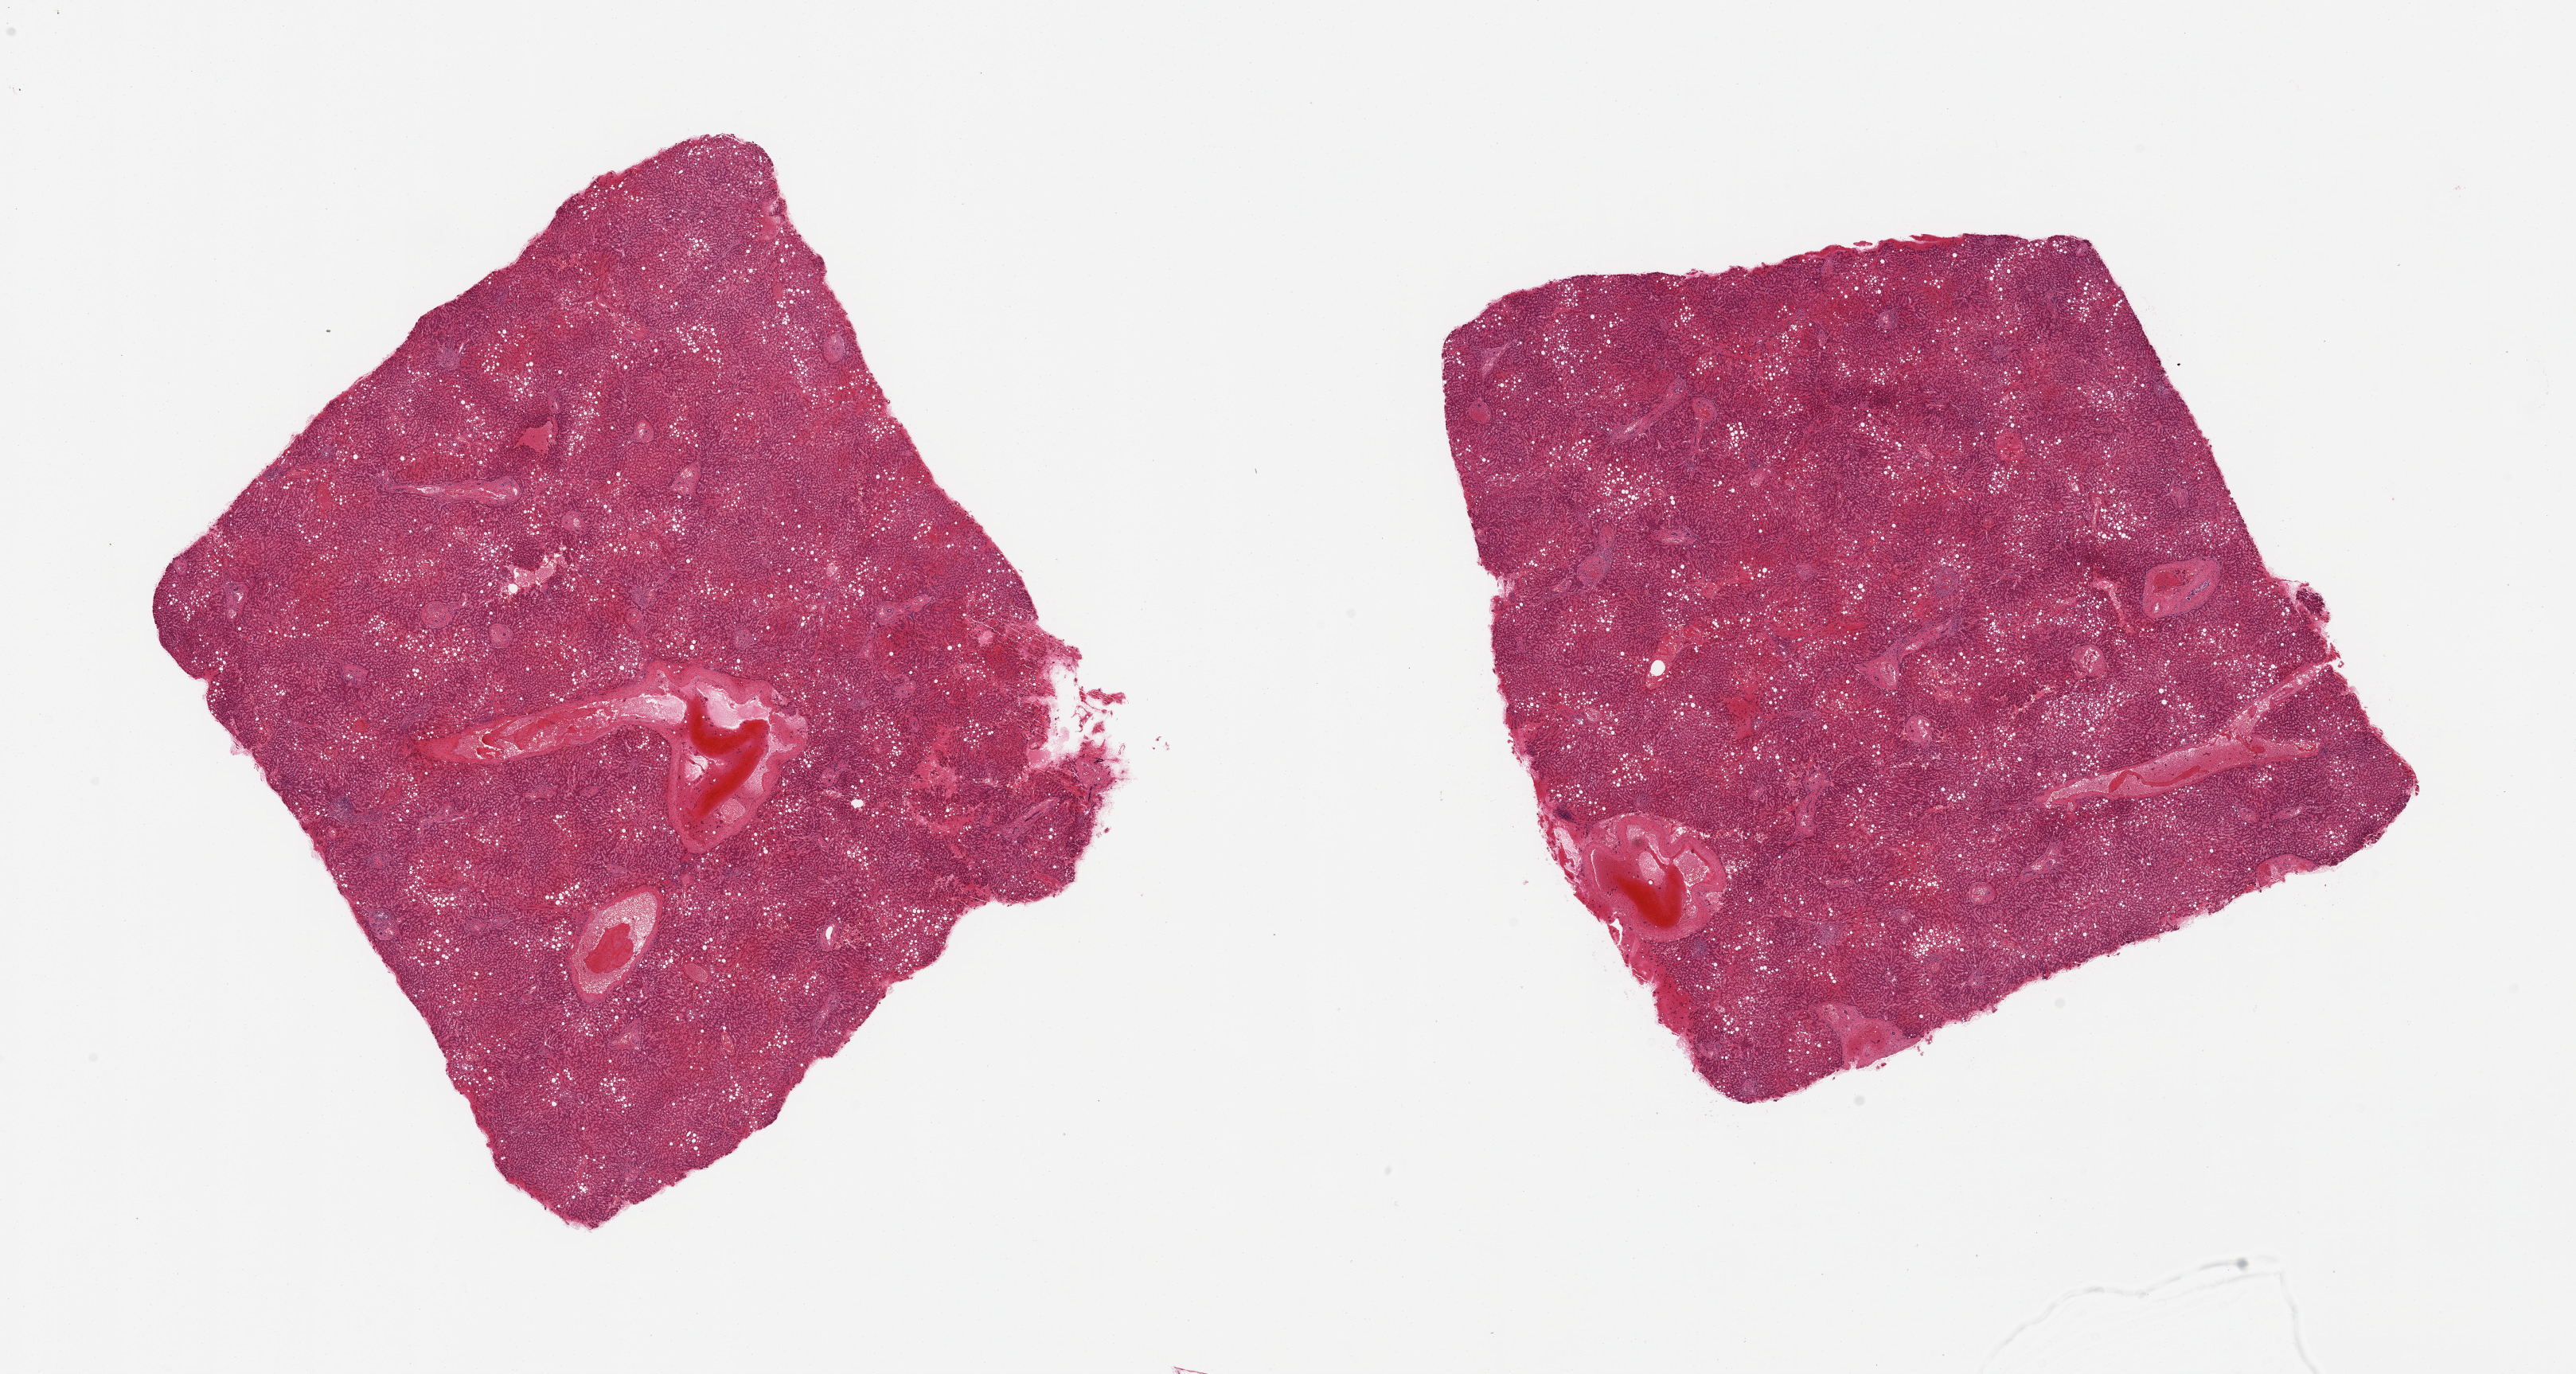
Whole-slide image, haematoxylin and eosin stain — low-resolution overview of the scanned area, about 25.6 x 13.7 mm (acquisition: 20x scan), PAXgene-fixed paraffin-embedded (PFPE) section, sampled site (target tissue): liver, tissue donor sample. Donor: male.
Review note (as recorded): 2 pieces; mild steatosis, passive congestion.